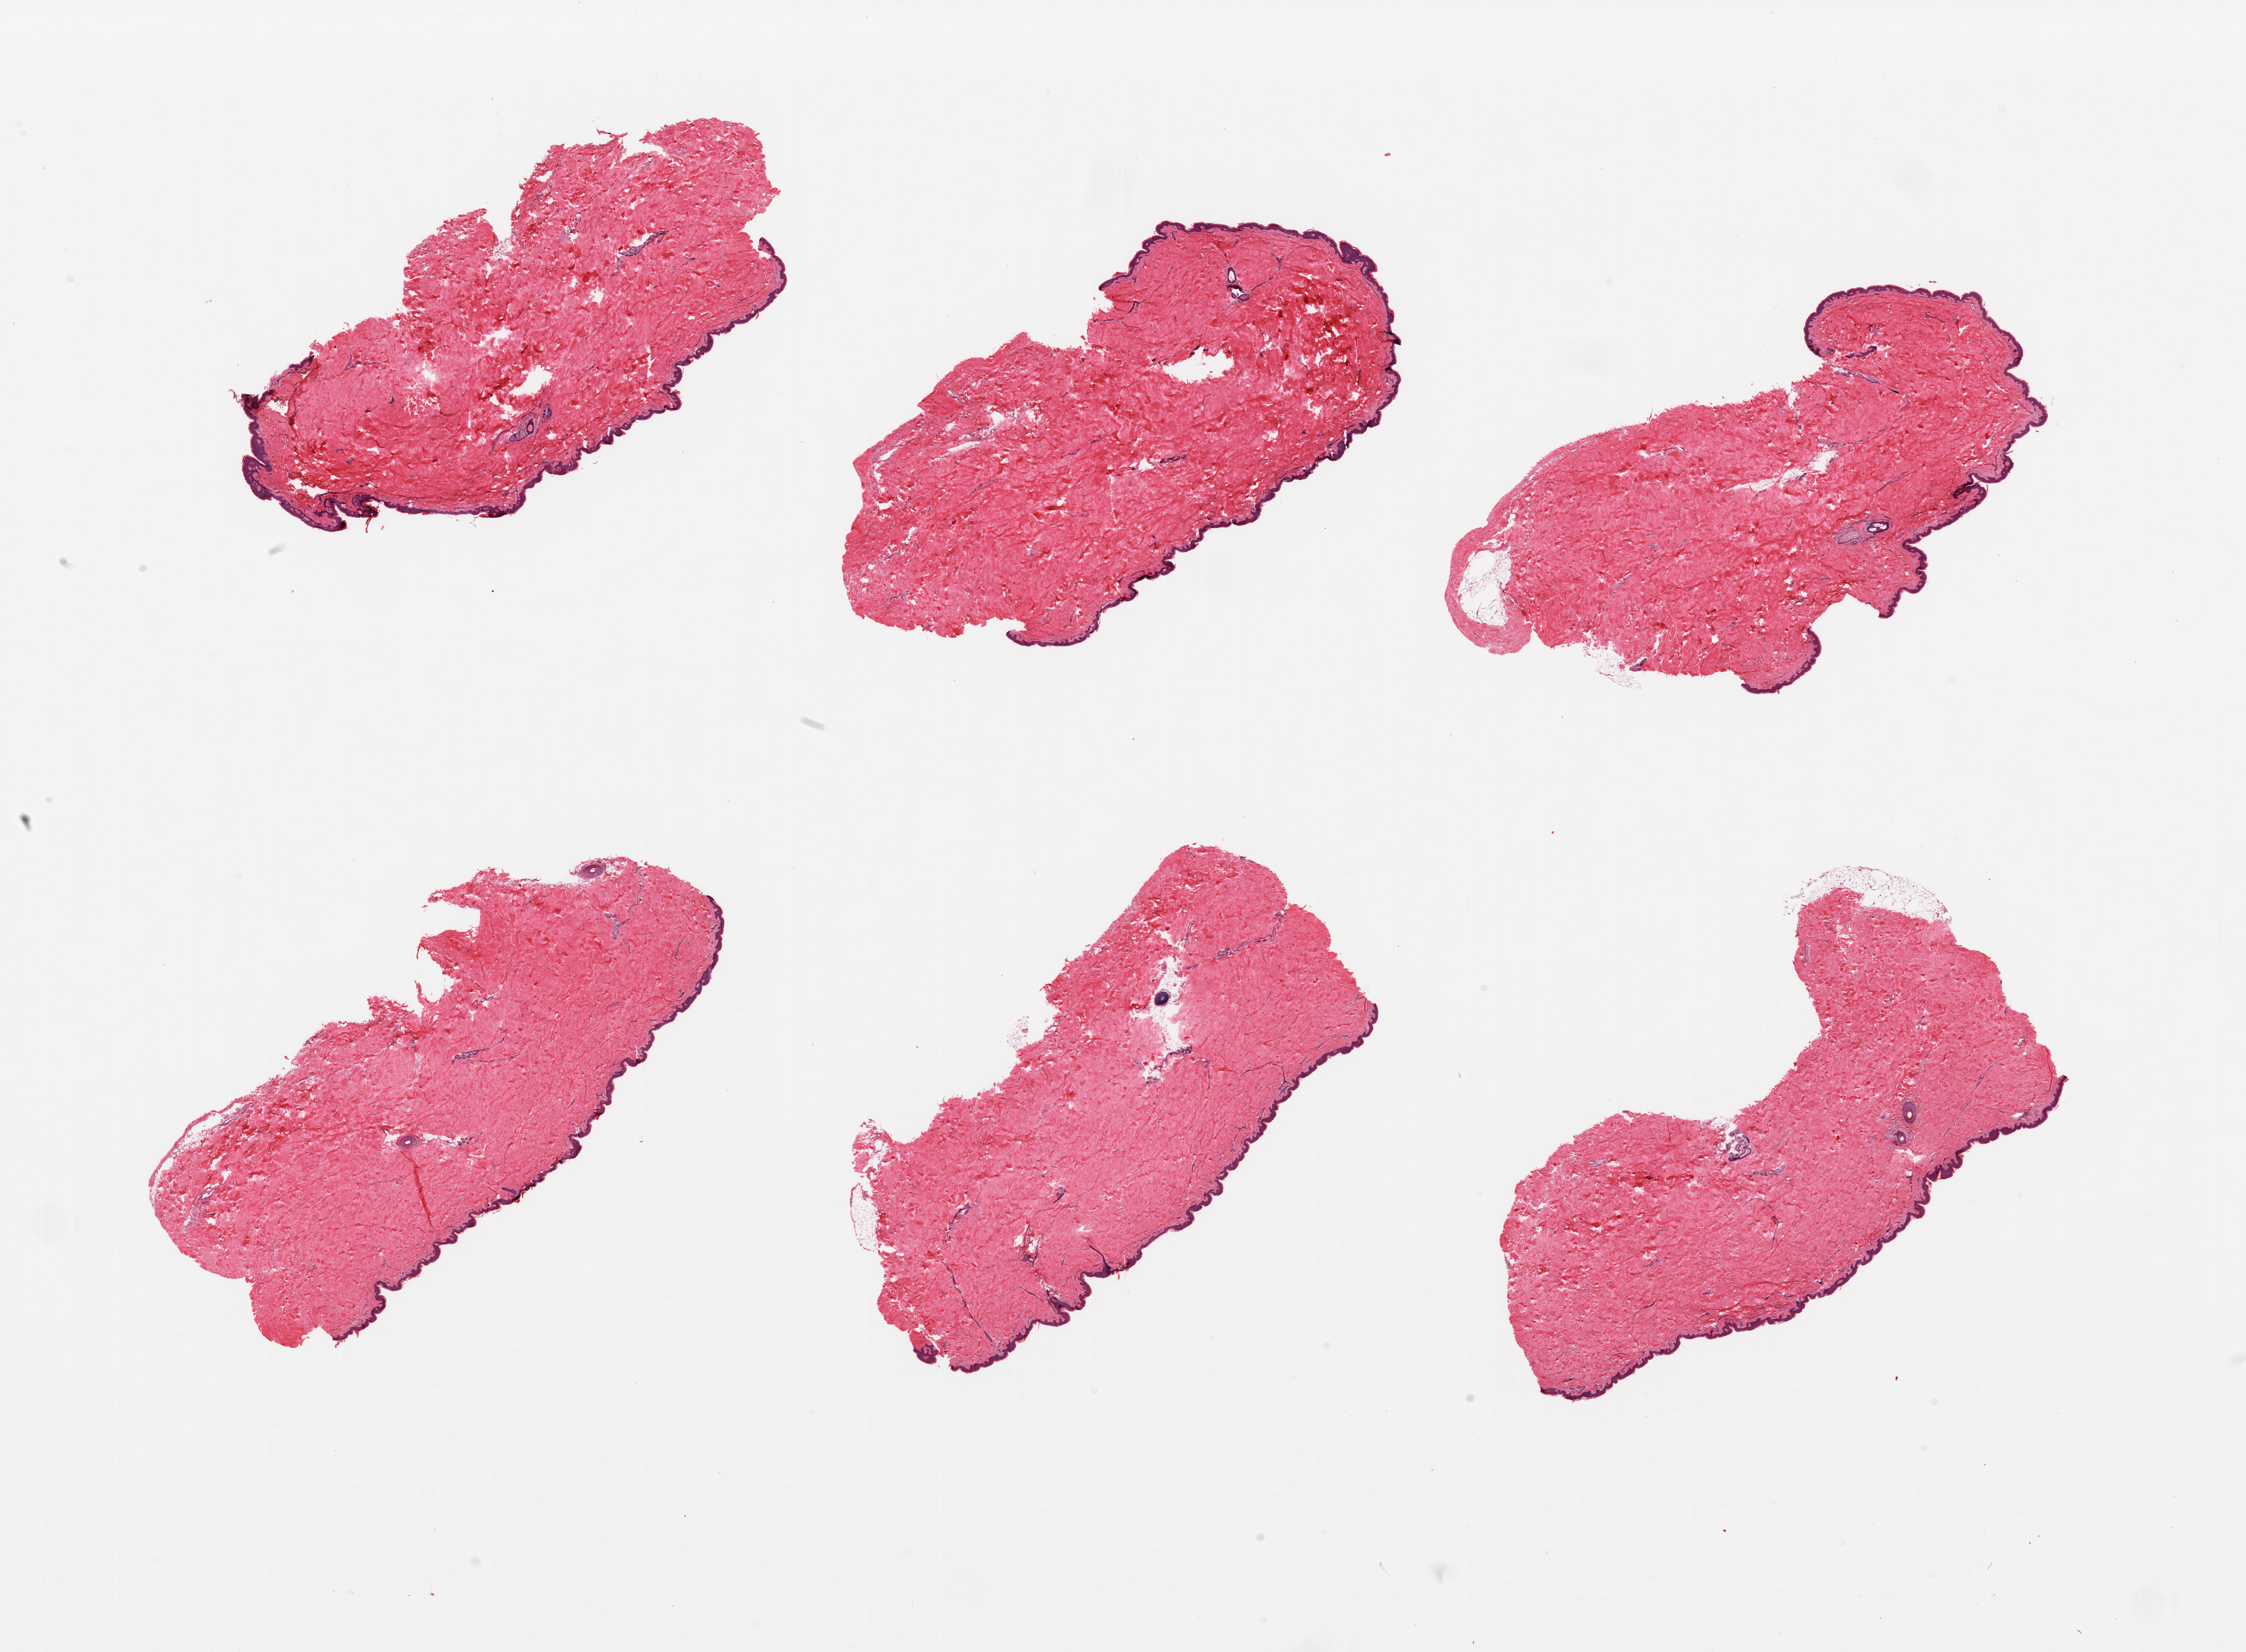
Haematoxylin and eosin whole-slide image, a low-resolution overview of the entire scanned area, about 29.5 x 21.7 mm (slide scanned at 20x). PAXgene-fixed paraffin-embedded (PFPE) section. Section of skin of suprapubic region (target tissue). Tissue donor sample.
- reviewer comment on this tissue sample: 6 pieces, minimal dermal fat, squamous epithelium is ~50-60 microns